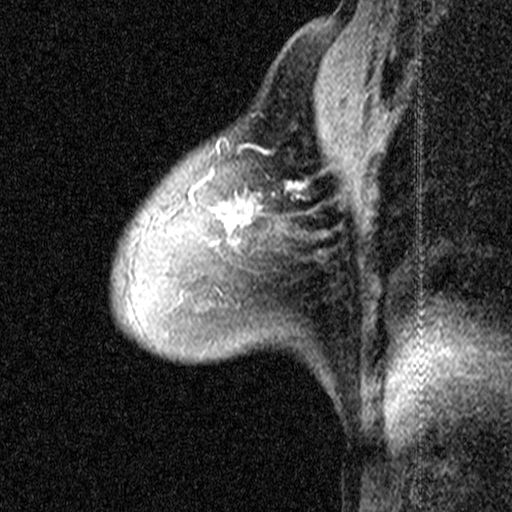
Breast MRI (dynamic contrast-enhanced), one sagittal slice. Slice 31 of 44 in the series (ordered by position). Dynamic contrast-enhanced study with each time point stored as its own series, time point 2 of 3 at this slice position (early post-contrast, ordered by acquisition time). 1.5 T. TE 4.5 ms, TR 11 ms. 3 mm slice thickness. 512 × 512 image matrix, field of view 200 × 200 mm. Patient: female, 53 years. Case-level facts recorded for this patient, not image findings: setting: breast cancer imaged before/during neoadjuvant chemotherapy; receptor status: HR-positive, HER2-negative.
Annotated regions visible in this slice (semi-automatically segmented with operator editing):
- analysis volume of interest (the breast-tissue region the enhancement analysis was run in; not a lesion): bounding box (x1, y1, x2, y2) in pixels: (198, 152, 299, 267)
- tumour enhancement mask (voxels above the 90 % enhancement threshold inside the analysis volume of interest): (217, 181, 299, 227)